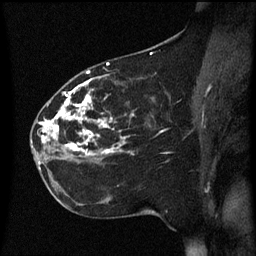
Breast MRI (dynamic contrast-enhanced), one sagittal slice. Slice 29 of 60 in the series (ordered by position). Dynamic contrast-enhanced series, image 2 of 3 at this slice position (ordered by acquisition). 1.5 T. TE 4.2 ms, TR 8.4 ms. 256 × 256 image matrix, field of view 200 × 200 mm. Female patient, age 35 years. From the clinical record (not read from this slice): setting: breast cancer imaged before/during neoadjuvant chemotherapy; receptor status: HER2-positive.
Annotated regions visible in this slice (semi-automatically segmented with operator editing):
- analysis volume of interest (the breast-tissue region the enhancement analysis was run in; not a lesion): bounding box <32,78,172,163> (left, top, right, bottom; pixels)
- tumour enhancement mask (voxels above the 70 % enhancement threshold inside the analysis volume of interest): <32,80,124,155>